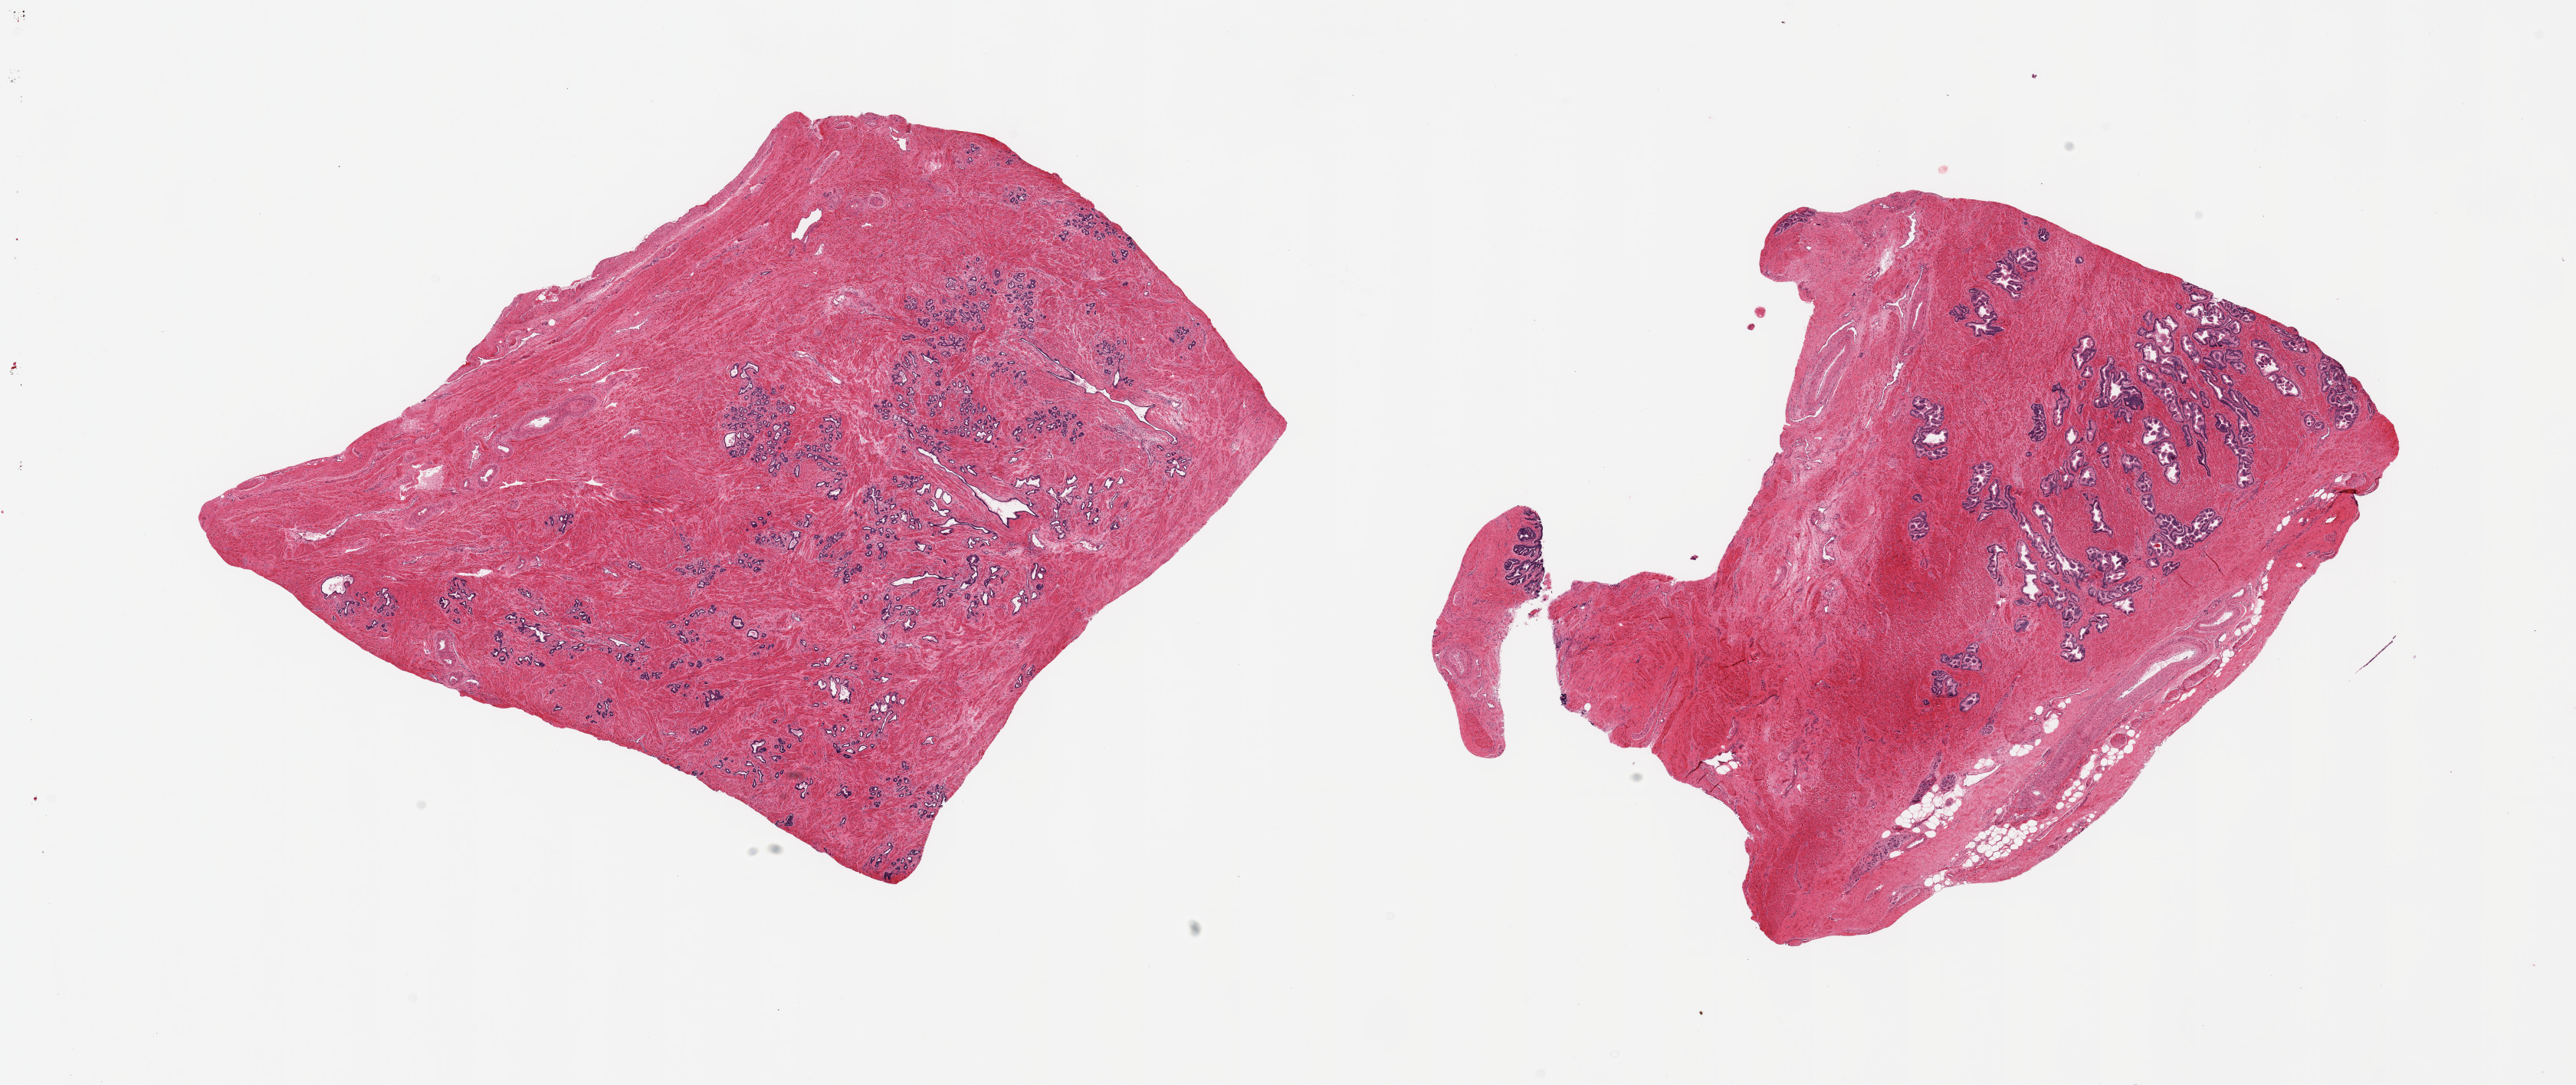
Whole-slide image, haematoxylin and eosin stain, brightfield, whole scanned area (about 26.6 x 11.2 mm, from a 20x scan) shown as a low-resolution overview, PAXgene-fixed, paraffin-embedded tissue, target tissue: prostate, donor tissue sample. Male donor.
Reviewer comment on this tissue sample: 2 pieces; includes small portion of seminal vesicle.